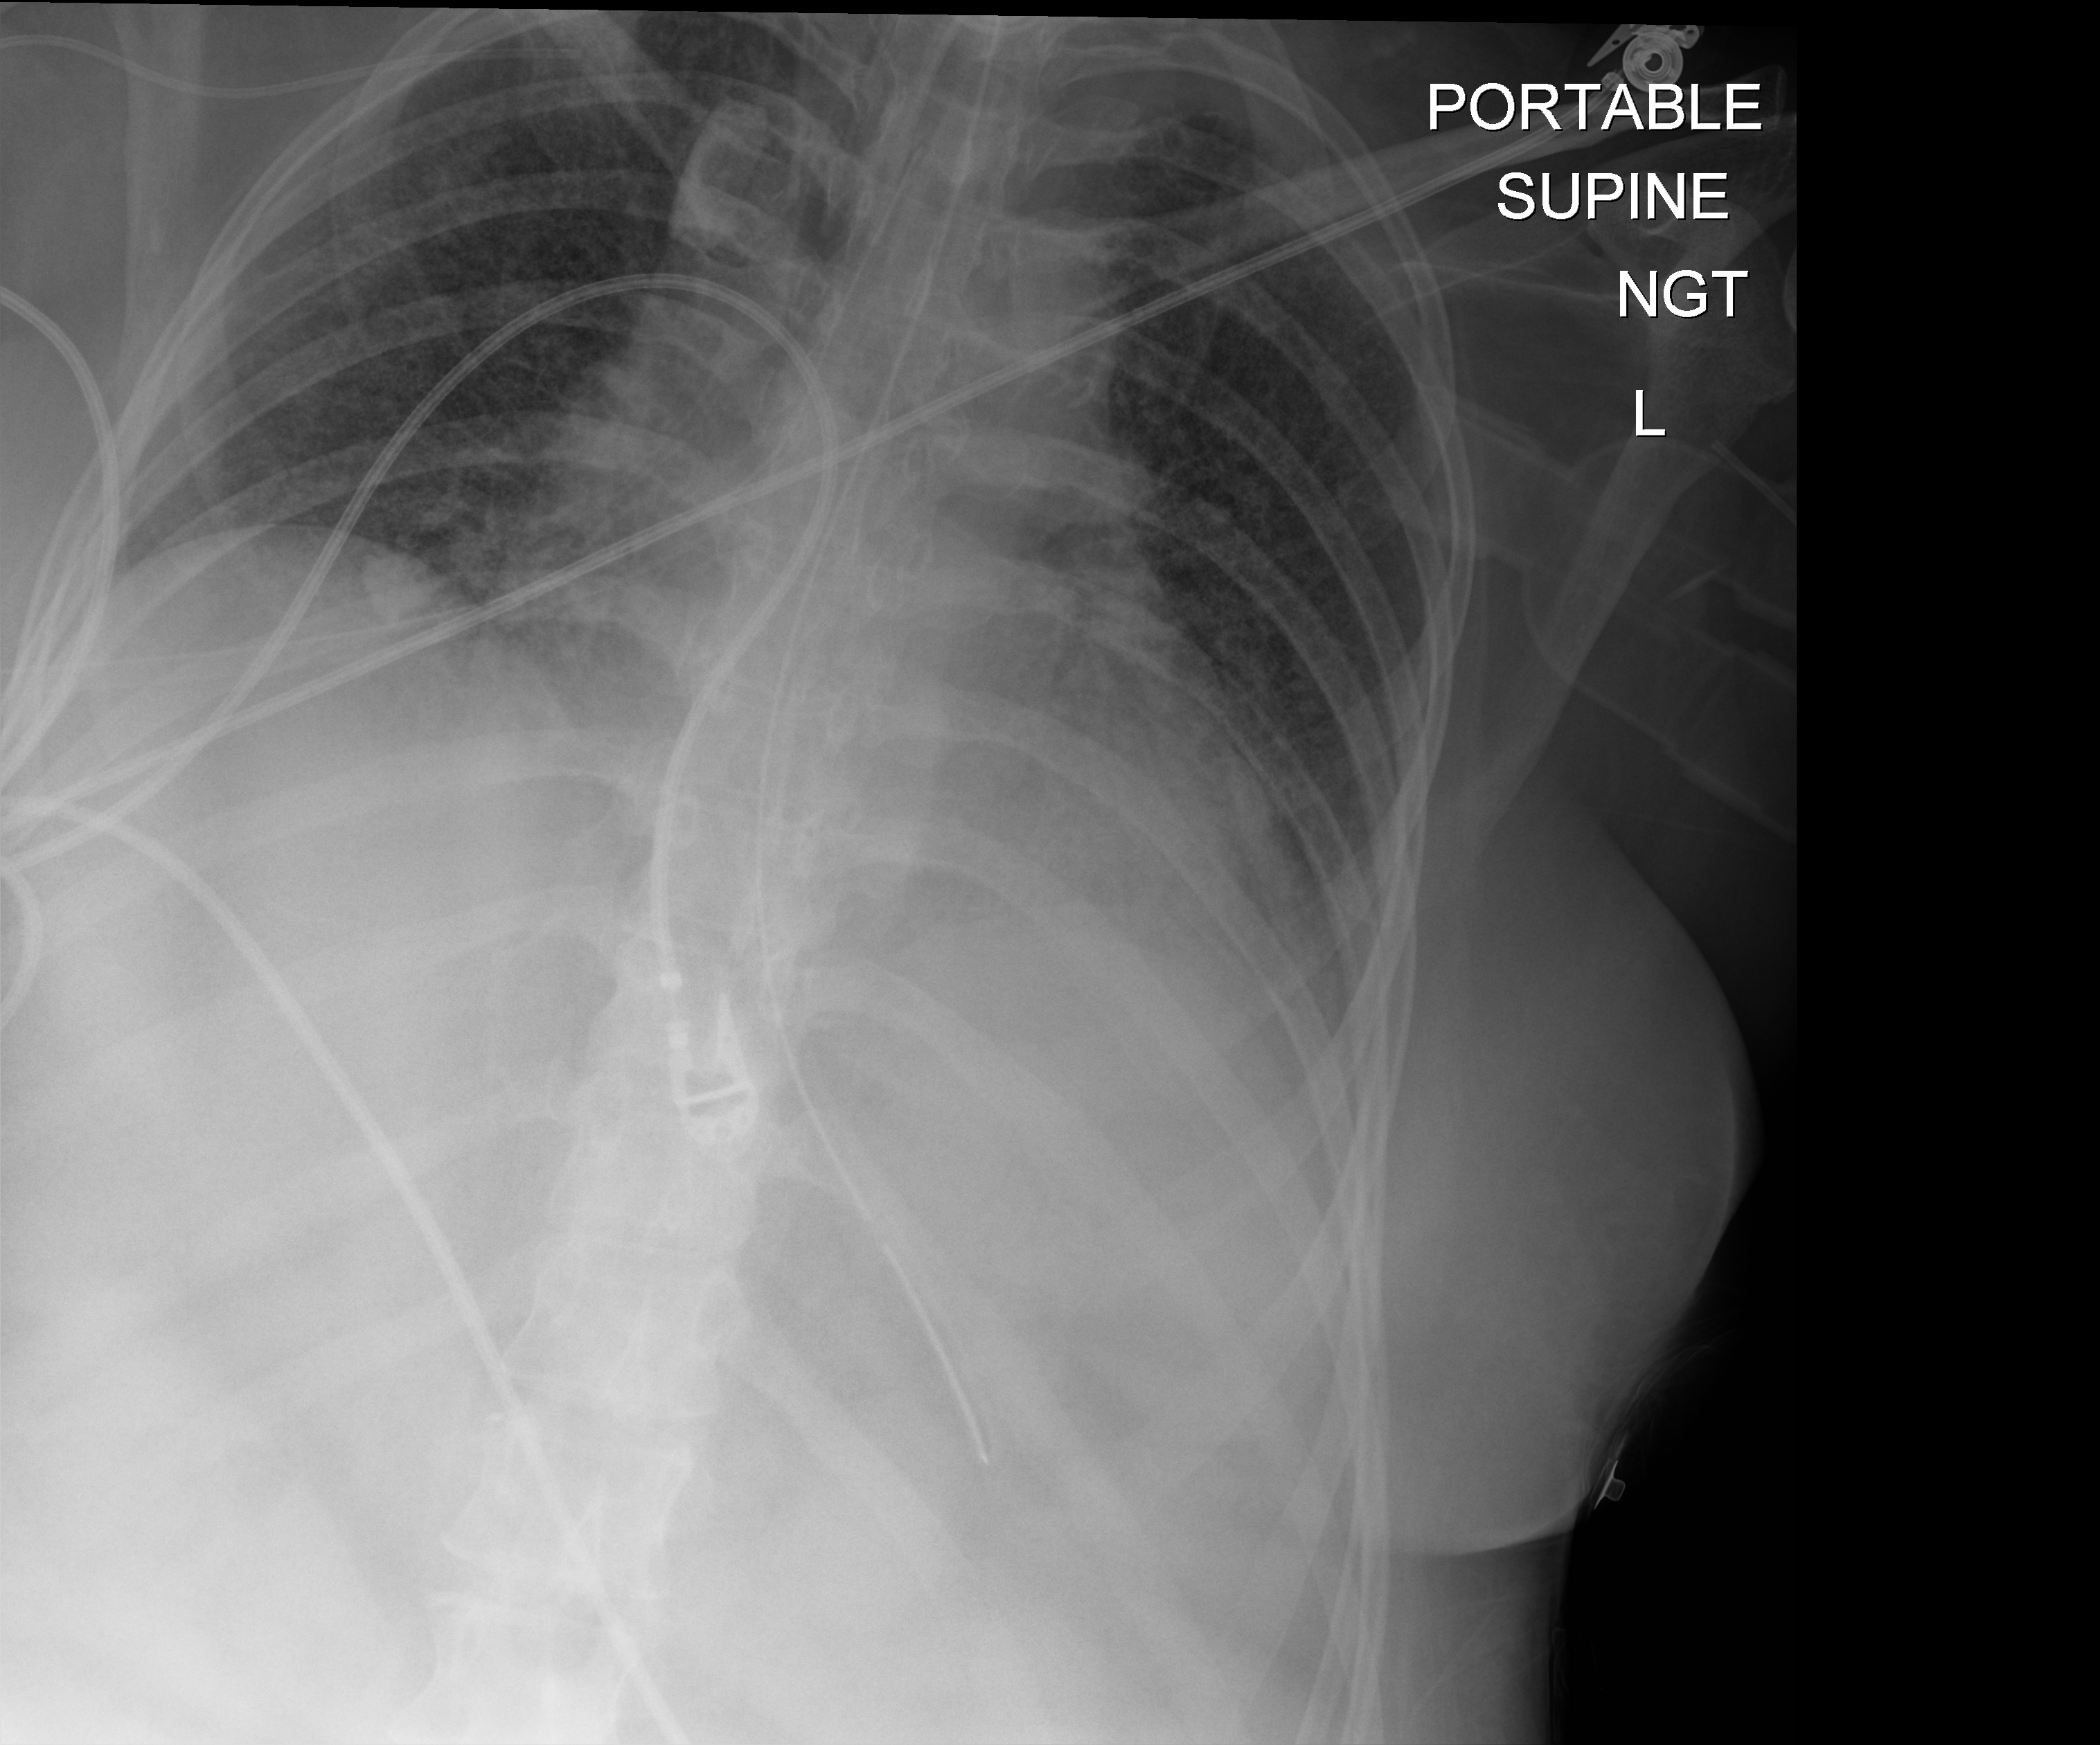
Chest X-ray (portable). Female patient hospitalised with COVID-19, age 18–59 years.
From the hospital-stay record, not from the radiograph (when in the stay this image was taken is not recorded): admitted to intensive care during this hospital stay: yes.